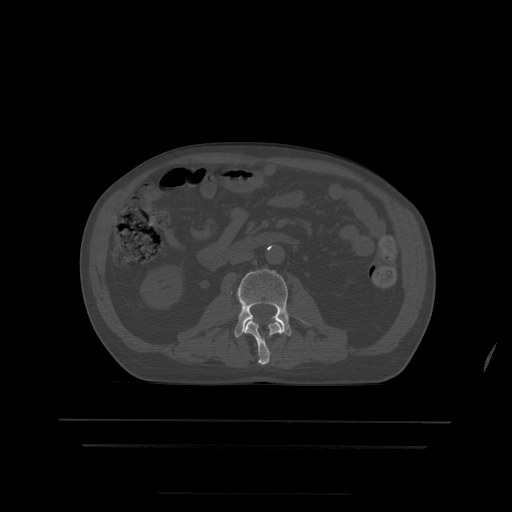
CT including the spine, one axial slice; position 129 of 522 along the scan axis; bone window (W 1800 / L 400 HU); 1.25 mm slice thickness; 512 × 512 image matrix. Patient age 68 years. Case-level facts recorded for this patient, not image findings: primary cancer: urothelial.
Outlined on this slice (semi-automatically segmented with operator editing):
- L2 vertebra: bounding box <245,321,282,365> (left, top, right, bottom; pixels)
- L3 vertebra: <223,269,292,338>